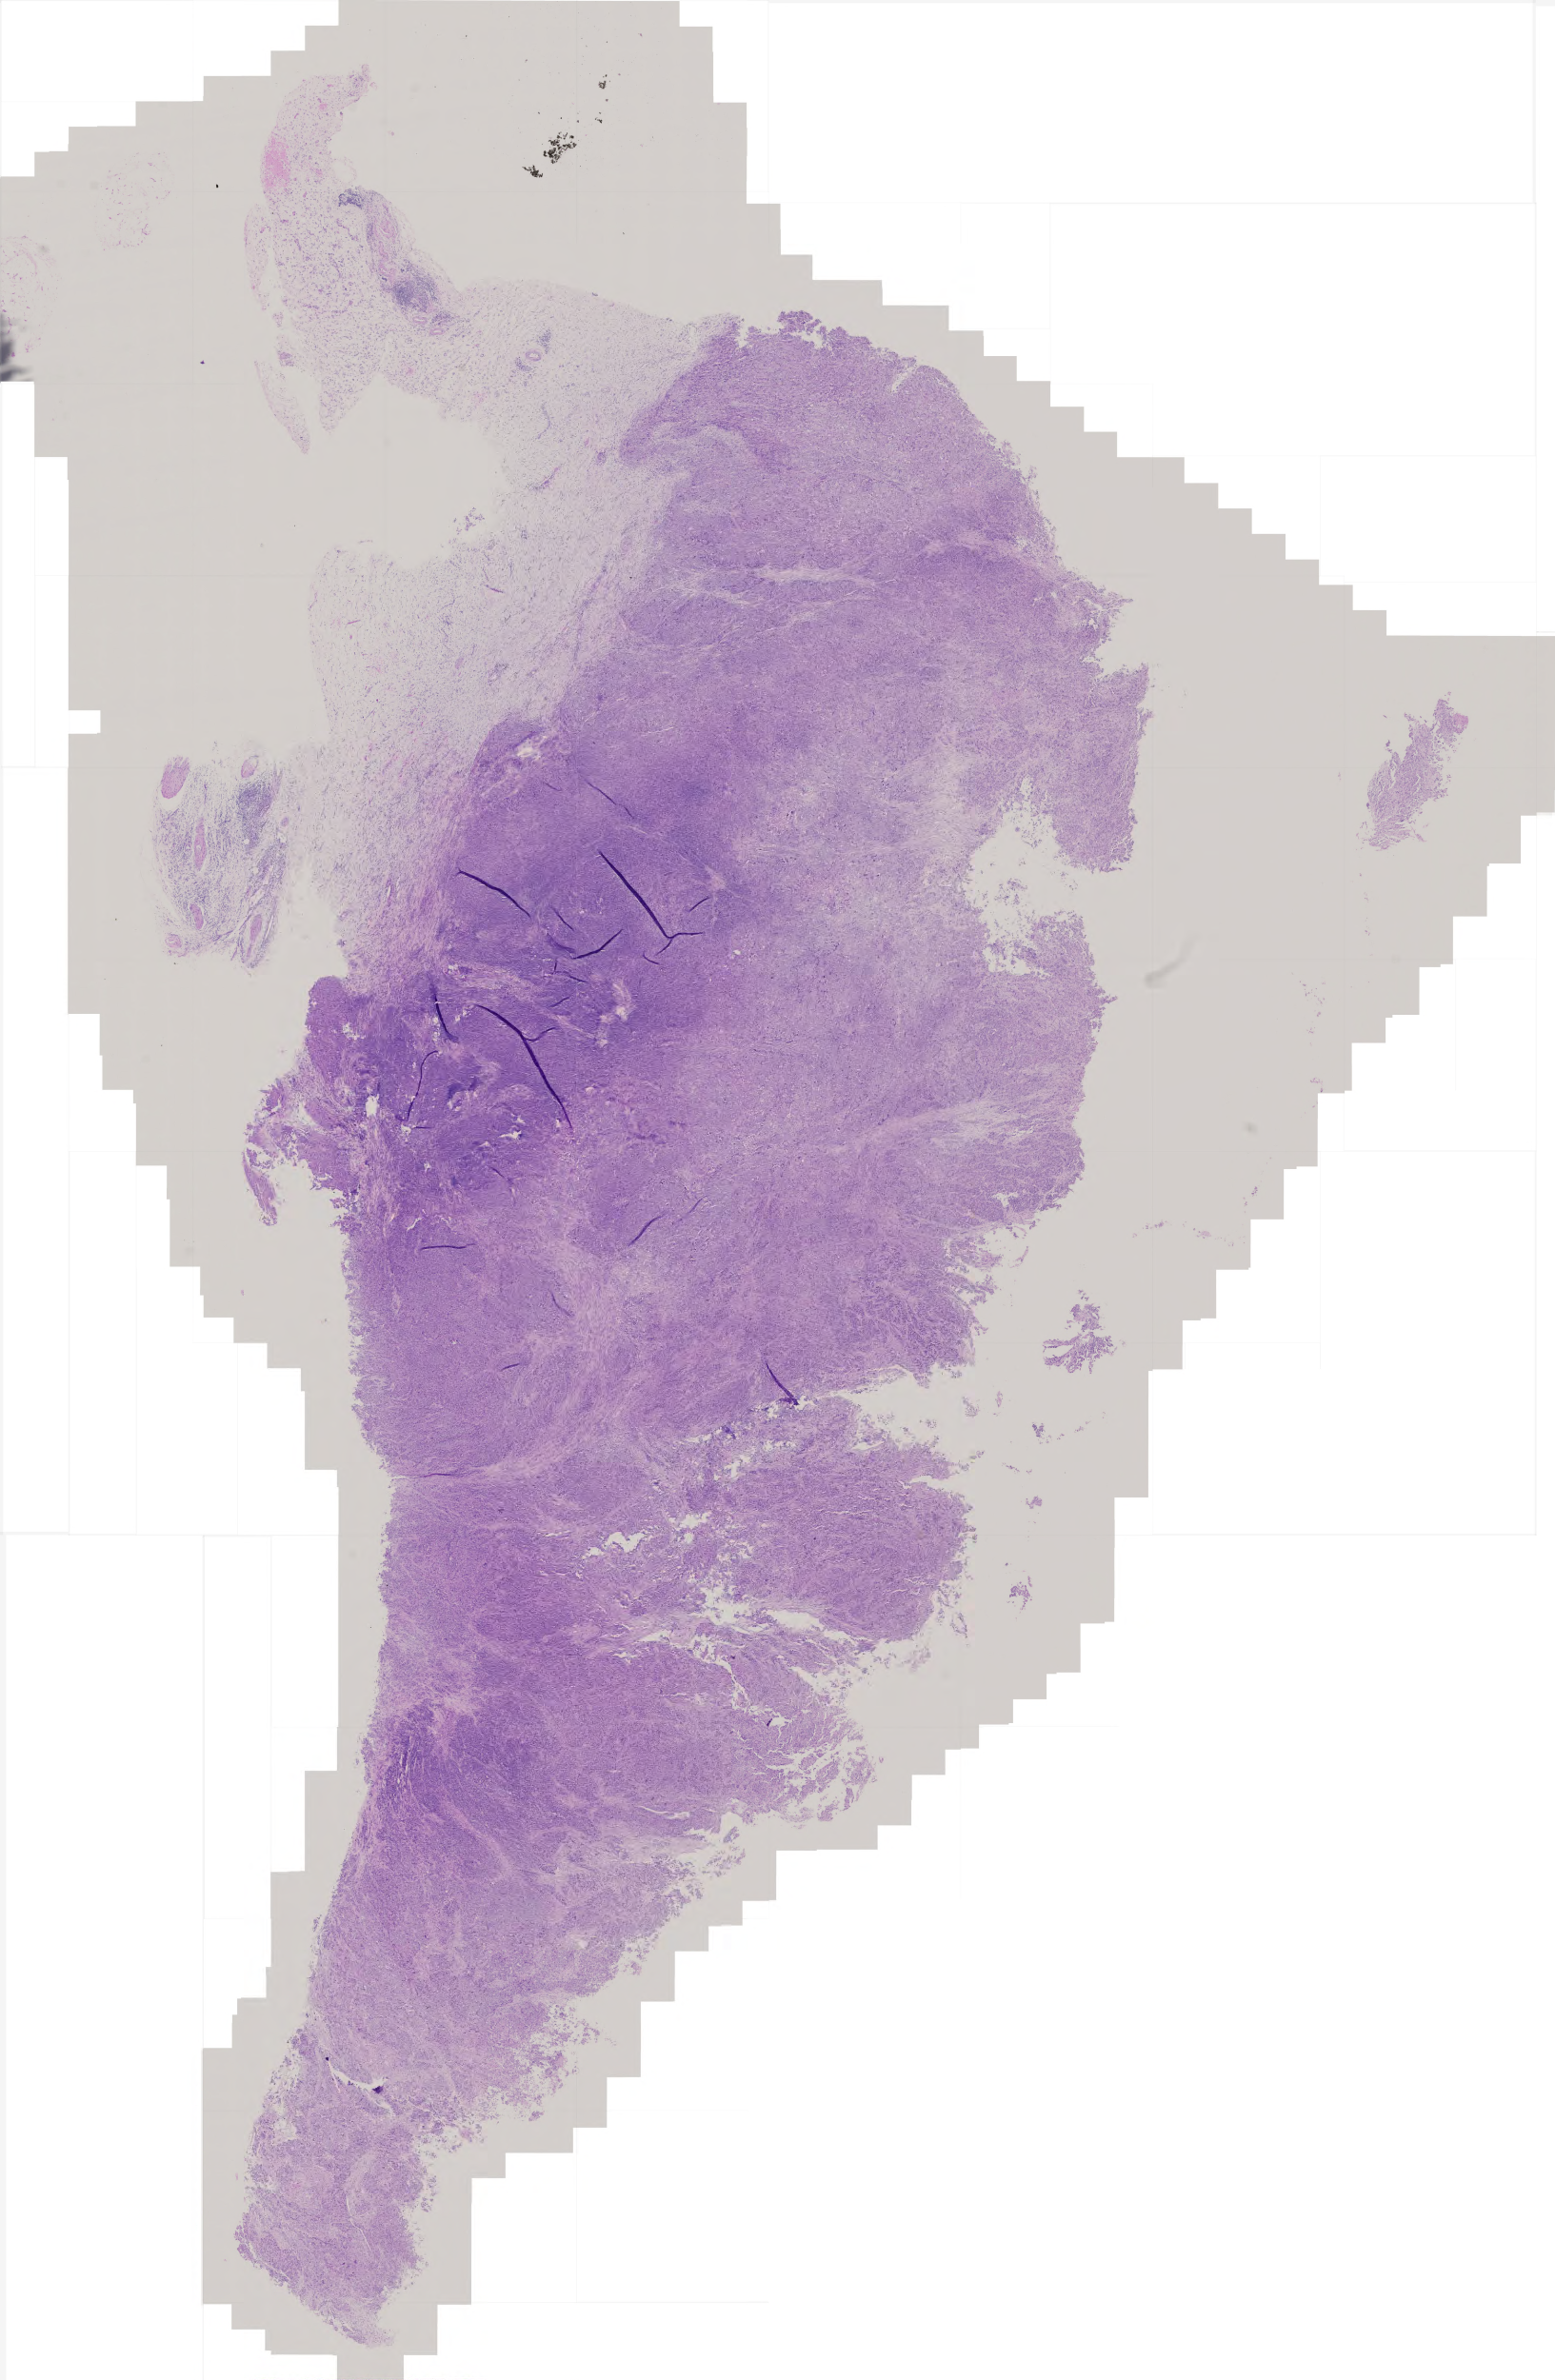
H&E whole-slide image, whole scanned area (about 3.3 x 5.0 mm) shown as a low-resolution overview. FFPE section. Stomach, primary tumour sample. Male, age 58 years at initial diagnosis. Histologic grade: G3 (poorly differentiated).
- AJCC pathologic stage: IV (5th edition)
- histologic diagnosis: Adenocarcinoma, intestinal type (gastric antrum)